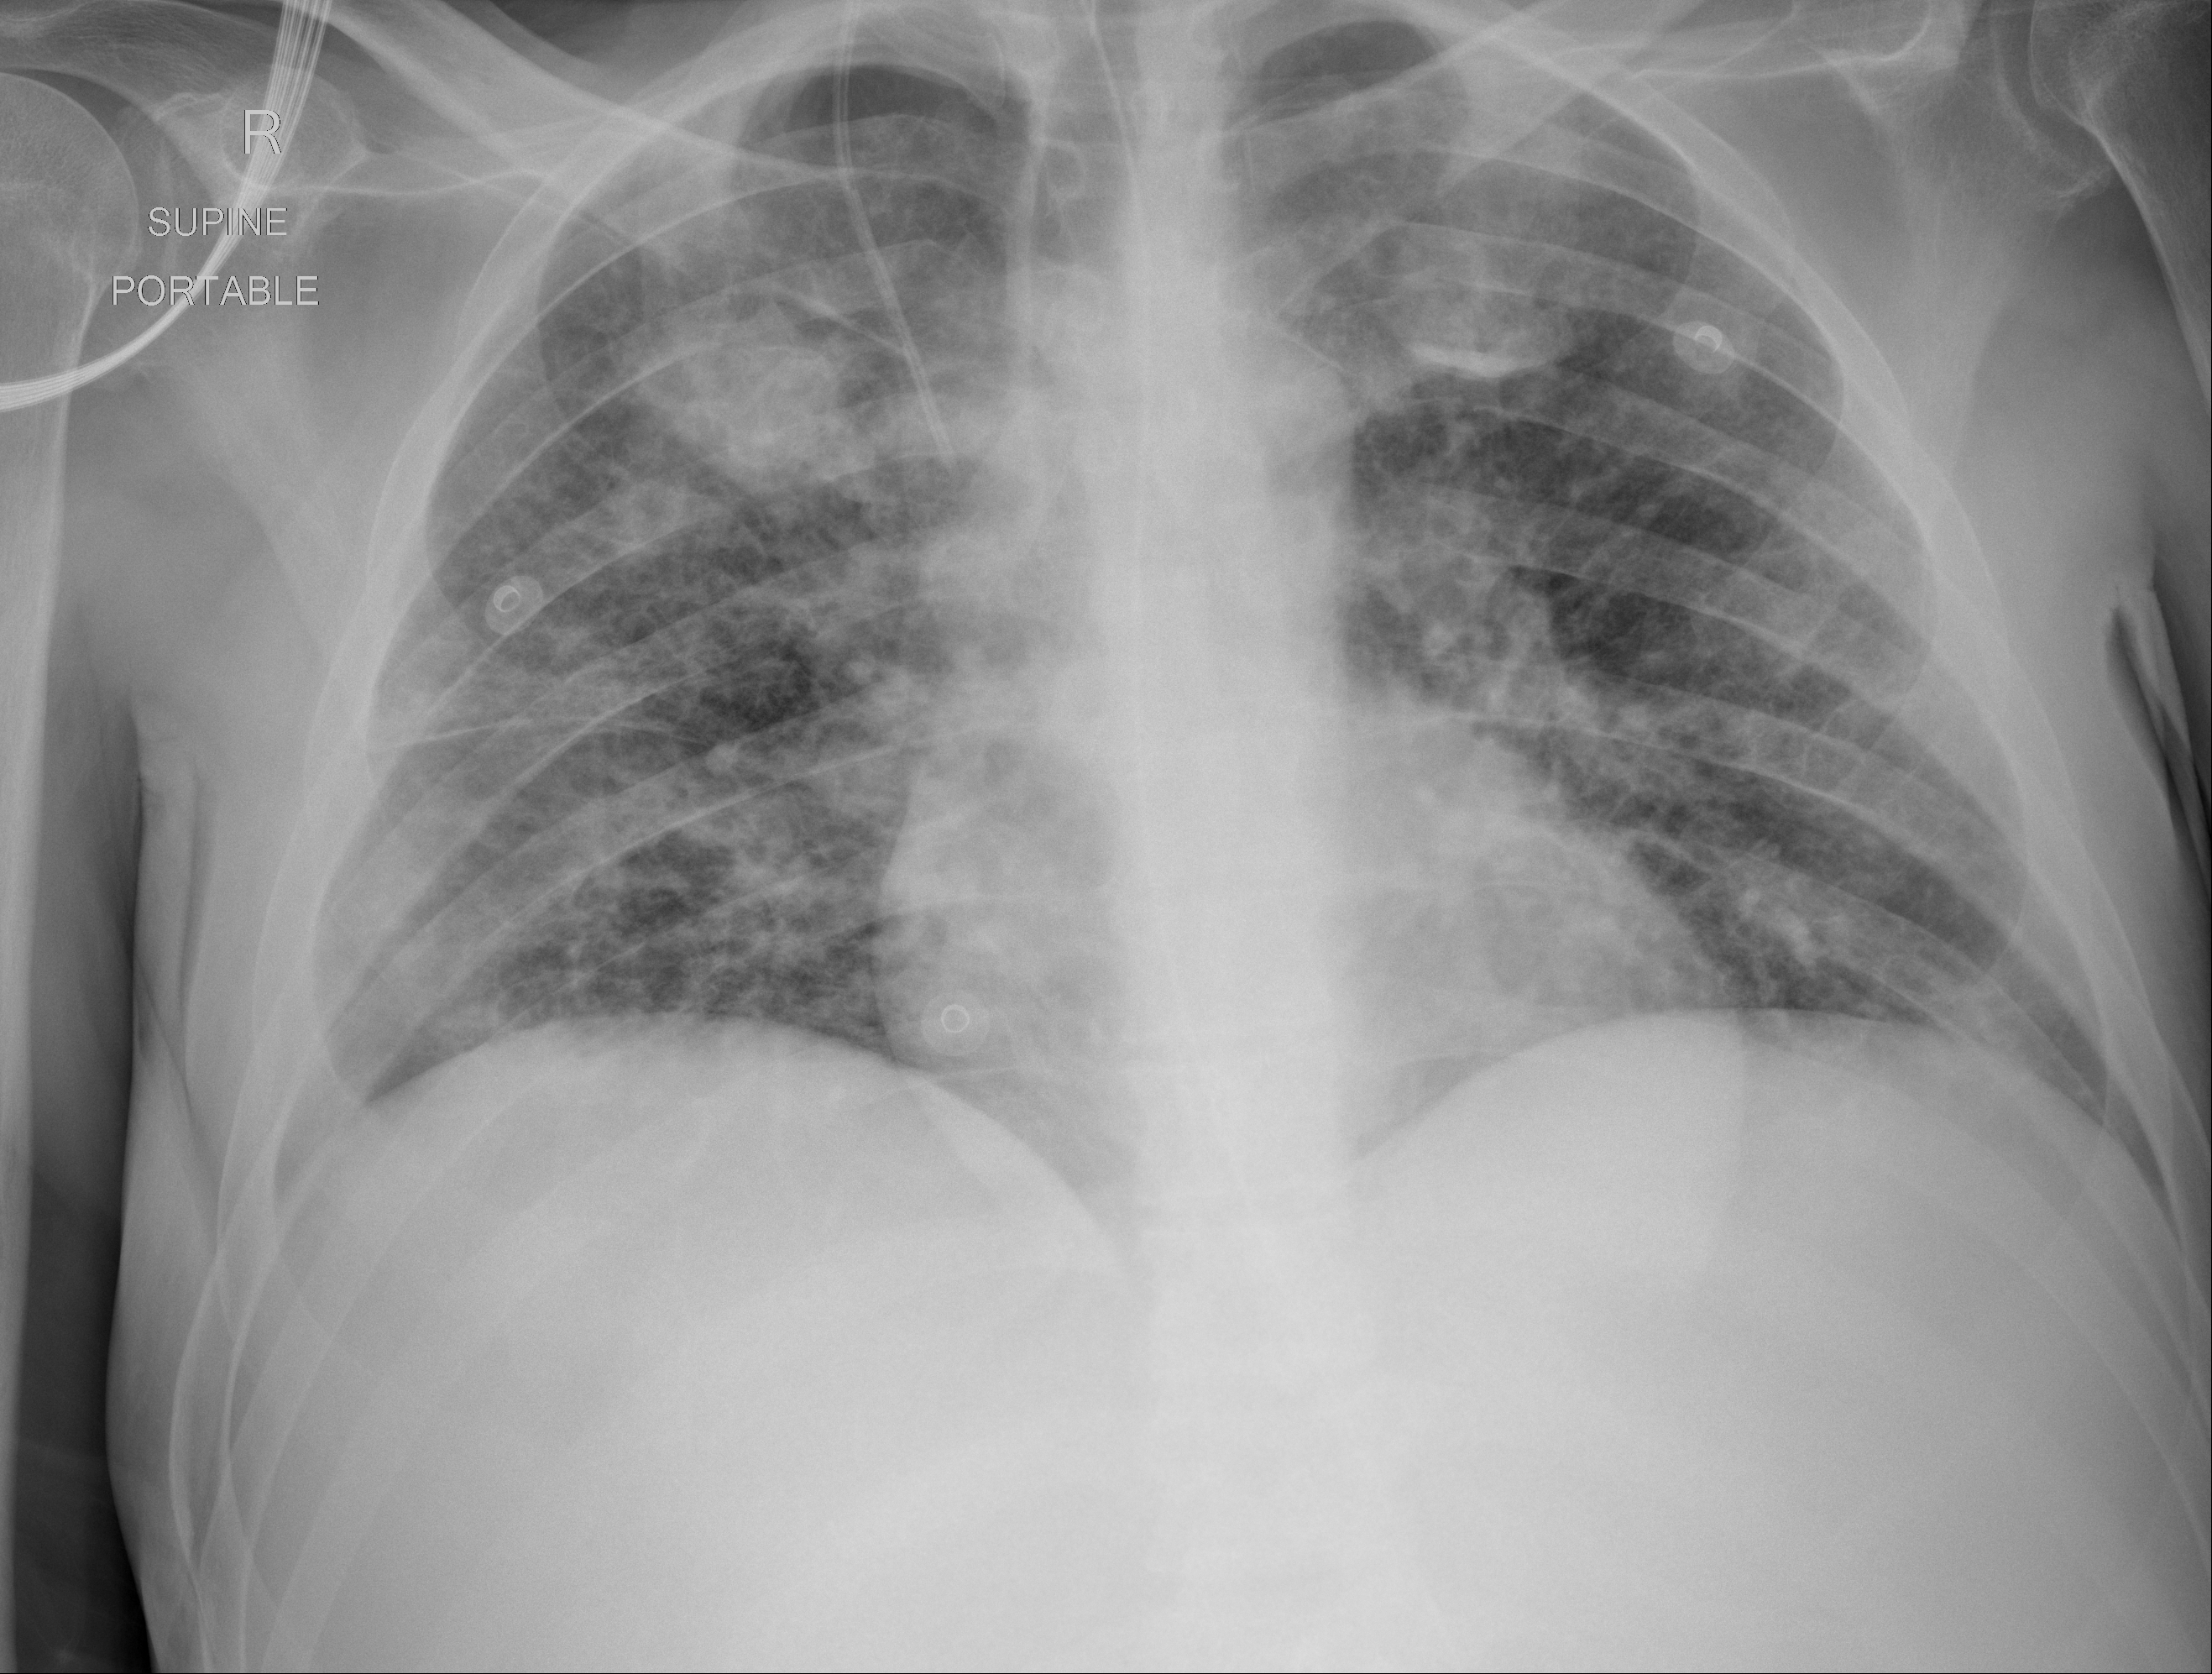
Portable chest radiograph, AP projection. Male patient, age 54 years; imaged 7 days after the COVID-19 diagnosis.
Key findings recorded by the radiologist: Interval improved aeration from previous exam. Patchy opacities throughout the right upper, mid, and bilateral lower lungs.